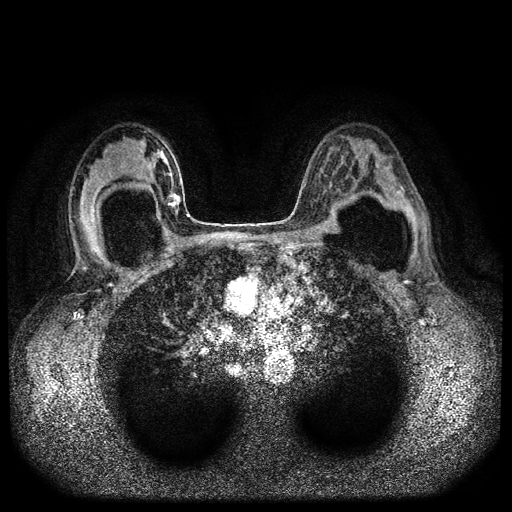
Breast MRI (dynamic contrast-enhanced, multi-phase), one axial slice; dynamic contrast-enhanced series, time point 2 of 5 at this slice position (early post-contrast); 1.5 T; TE 2.6 ms, TR 5.4 ms; 2 mm slice thickness; 512 × 512 image matrix. Female patient, age 42 years.
Outlined on this slice (semi-automatic segmentation, software-assisted and operator-edited):
- breast lesion (labelled 'tumour' in the annotation; benign lesions carry a separate 'benign' label): bounding box <165,192,182,209> (left, top, right, bottom; pixels)